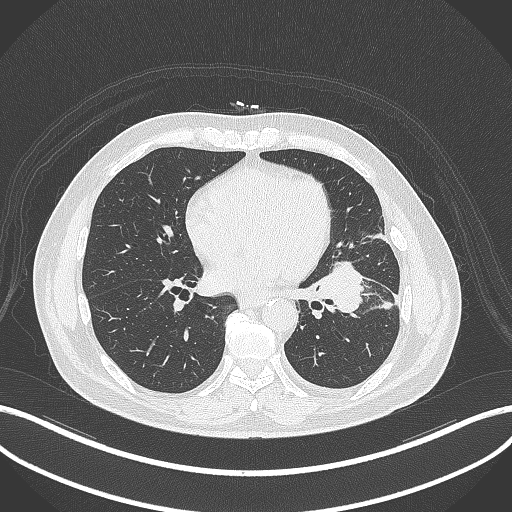
Chest CT, one axial slice; slice 154 of 230 in the series (ordered by position); lung window (W 1500 / L -600 HU); 512 × 512 image matrix, field of view 400 × 400 mm. Male patient, age 68 years. Case-level facts recorded for this patient, not image findings: clinical TNM (as recorded): T2b N0 M0.
Annotated regions visible in this slice (bounding box drawn by a radiologist):
- lung tumour (recorded histology: squamous cell carcinoma): box from (x=308, y=254) to (x=369, y=321) px